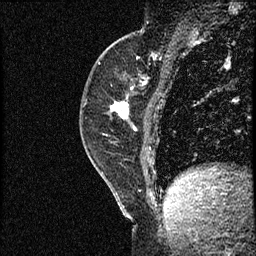
Breast MRI (dynamic contrast-enhanced), one sagittal slice. Slice 24 of 56 in the series (ordered by position). Dynamic contrast-enhanced study with each time point stored as its own series, time point 2 of 3 at this slice position (early post-contrast, ordered by acquisition time). 1.5 T. TE 4.2 ms, TR 17.3 ms. 2 mm slice thickness. 256 × 256 image matrix, field of view 200 × 200 mm. Female patient. From the clinical record (not read from this slice): setting: breast cancer imaged before/during neoadjuvant chemotherapy; receptor status: HER2-positive.
Structures marked on this image (semi-automatic segmentation, software-assisted and operator-edited):
- analysis volume of interest (the breast-tissue region the enhancement analysis was run in; not a lesion): box from (x=79, y=50) to (x=156, y=155) px
- tumour enhancement mask (voxels above the 100 % enhancement threshold inside the analysis volume of interest): (x=111, y=102)–(x=136, y=130)